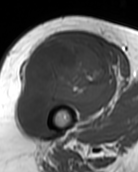
MRI of an extremity soft-tissue mass, one axial slice; slice 65 of 99 in the series (ordered by position); MR volume resampled by the dataset authors to the PET/CT grid (not the native acquisition matrix); 138 × 172 image matrix. Female patient. Case-level facts recorded for this patient, not image findings: histological type: pleiomorphic undifferentiated sarcoma; grade: high; site of the primary tumour: right quadricep.
Structures marked on this image (expert contour drawn on MRI and transferred to this co-registered scan by the dataset authors):
- gross tumour volume including surrounding oedema: box from (x=18, y=38) to (x=111, y=128) px
- gross tumour volume (mass): (x=18, y=38)–(x=111, y=128)